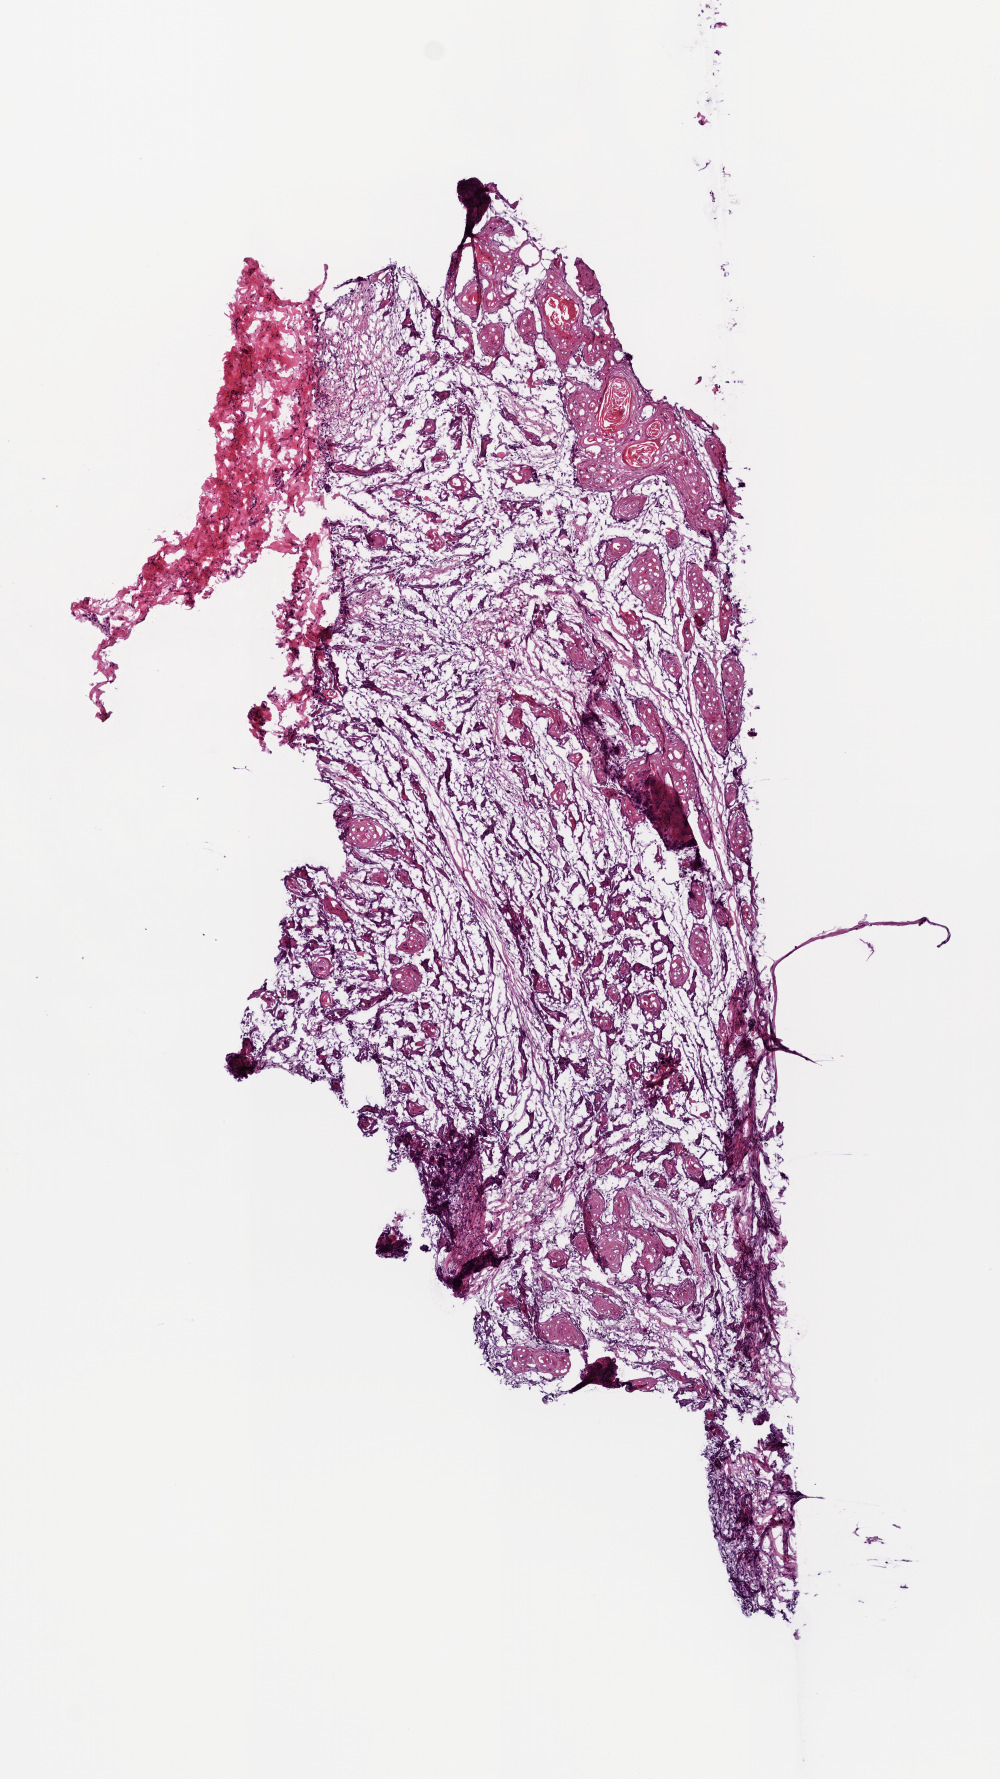
Digitized H&E-stained tissue section (whole slide), a low-resolution overview of the entire scanned area, about 4.0 x 7.1 mm (slide scanned at 20x); frozen section from the bottom of the tissue portion; primary tumour sample from the head and neck. Patient: male, age at initial diagnosis 64 years. Histologic grade: G3 (poorly differentiated). Composition of this section per pathologist review: tumour cells 30%, tumour nuclei 60%, normal cells 0%, stromal cells 70%, necrosis 0%.
* AJCC pathologic stage: IVA (7th edition)
* histologic diagnosis: Squamous cell carcinoma, NOS (larynx, NOS)